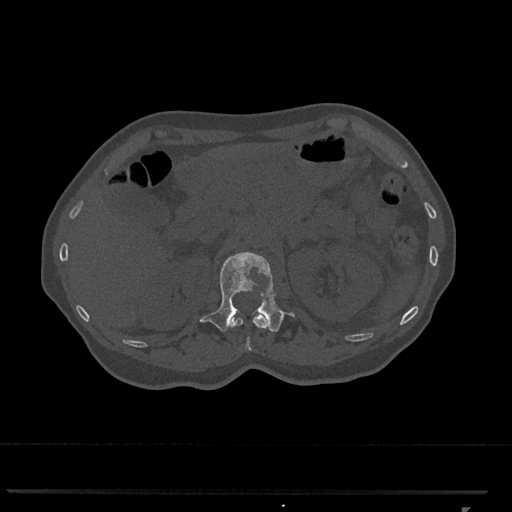
CT including the spine, one axial slice; position 419 of 793 along the scan axis; reconstruction kernel Br40s/3; 120 kVp; bone window (W 1800 / L 400 HU); 512 × 512 image matrix. Patient: female, 62 years. Case-level facts recorded for this patient, not image findings: primary cancer: renal.
Annotated regions visible in this slice (semi-automatic segmentation, software-assisted and operator-edited):
- L1 vertebra: bounding box (x1, y1, x2, y2) in pixels: (200, 252, 295, 332)
- T12 vertebra: (229, 313, 267, 351)